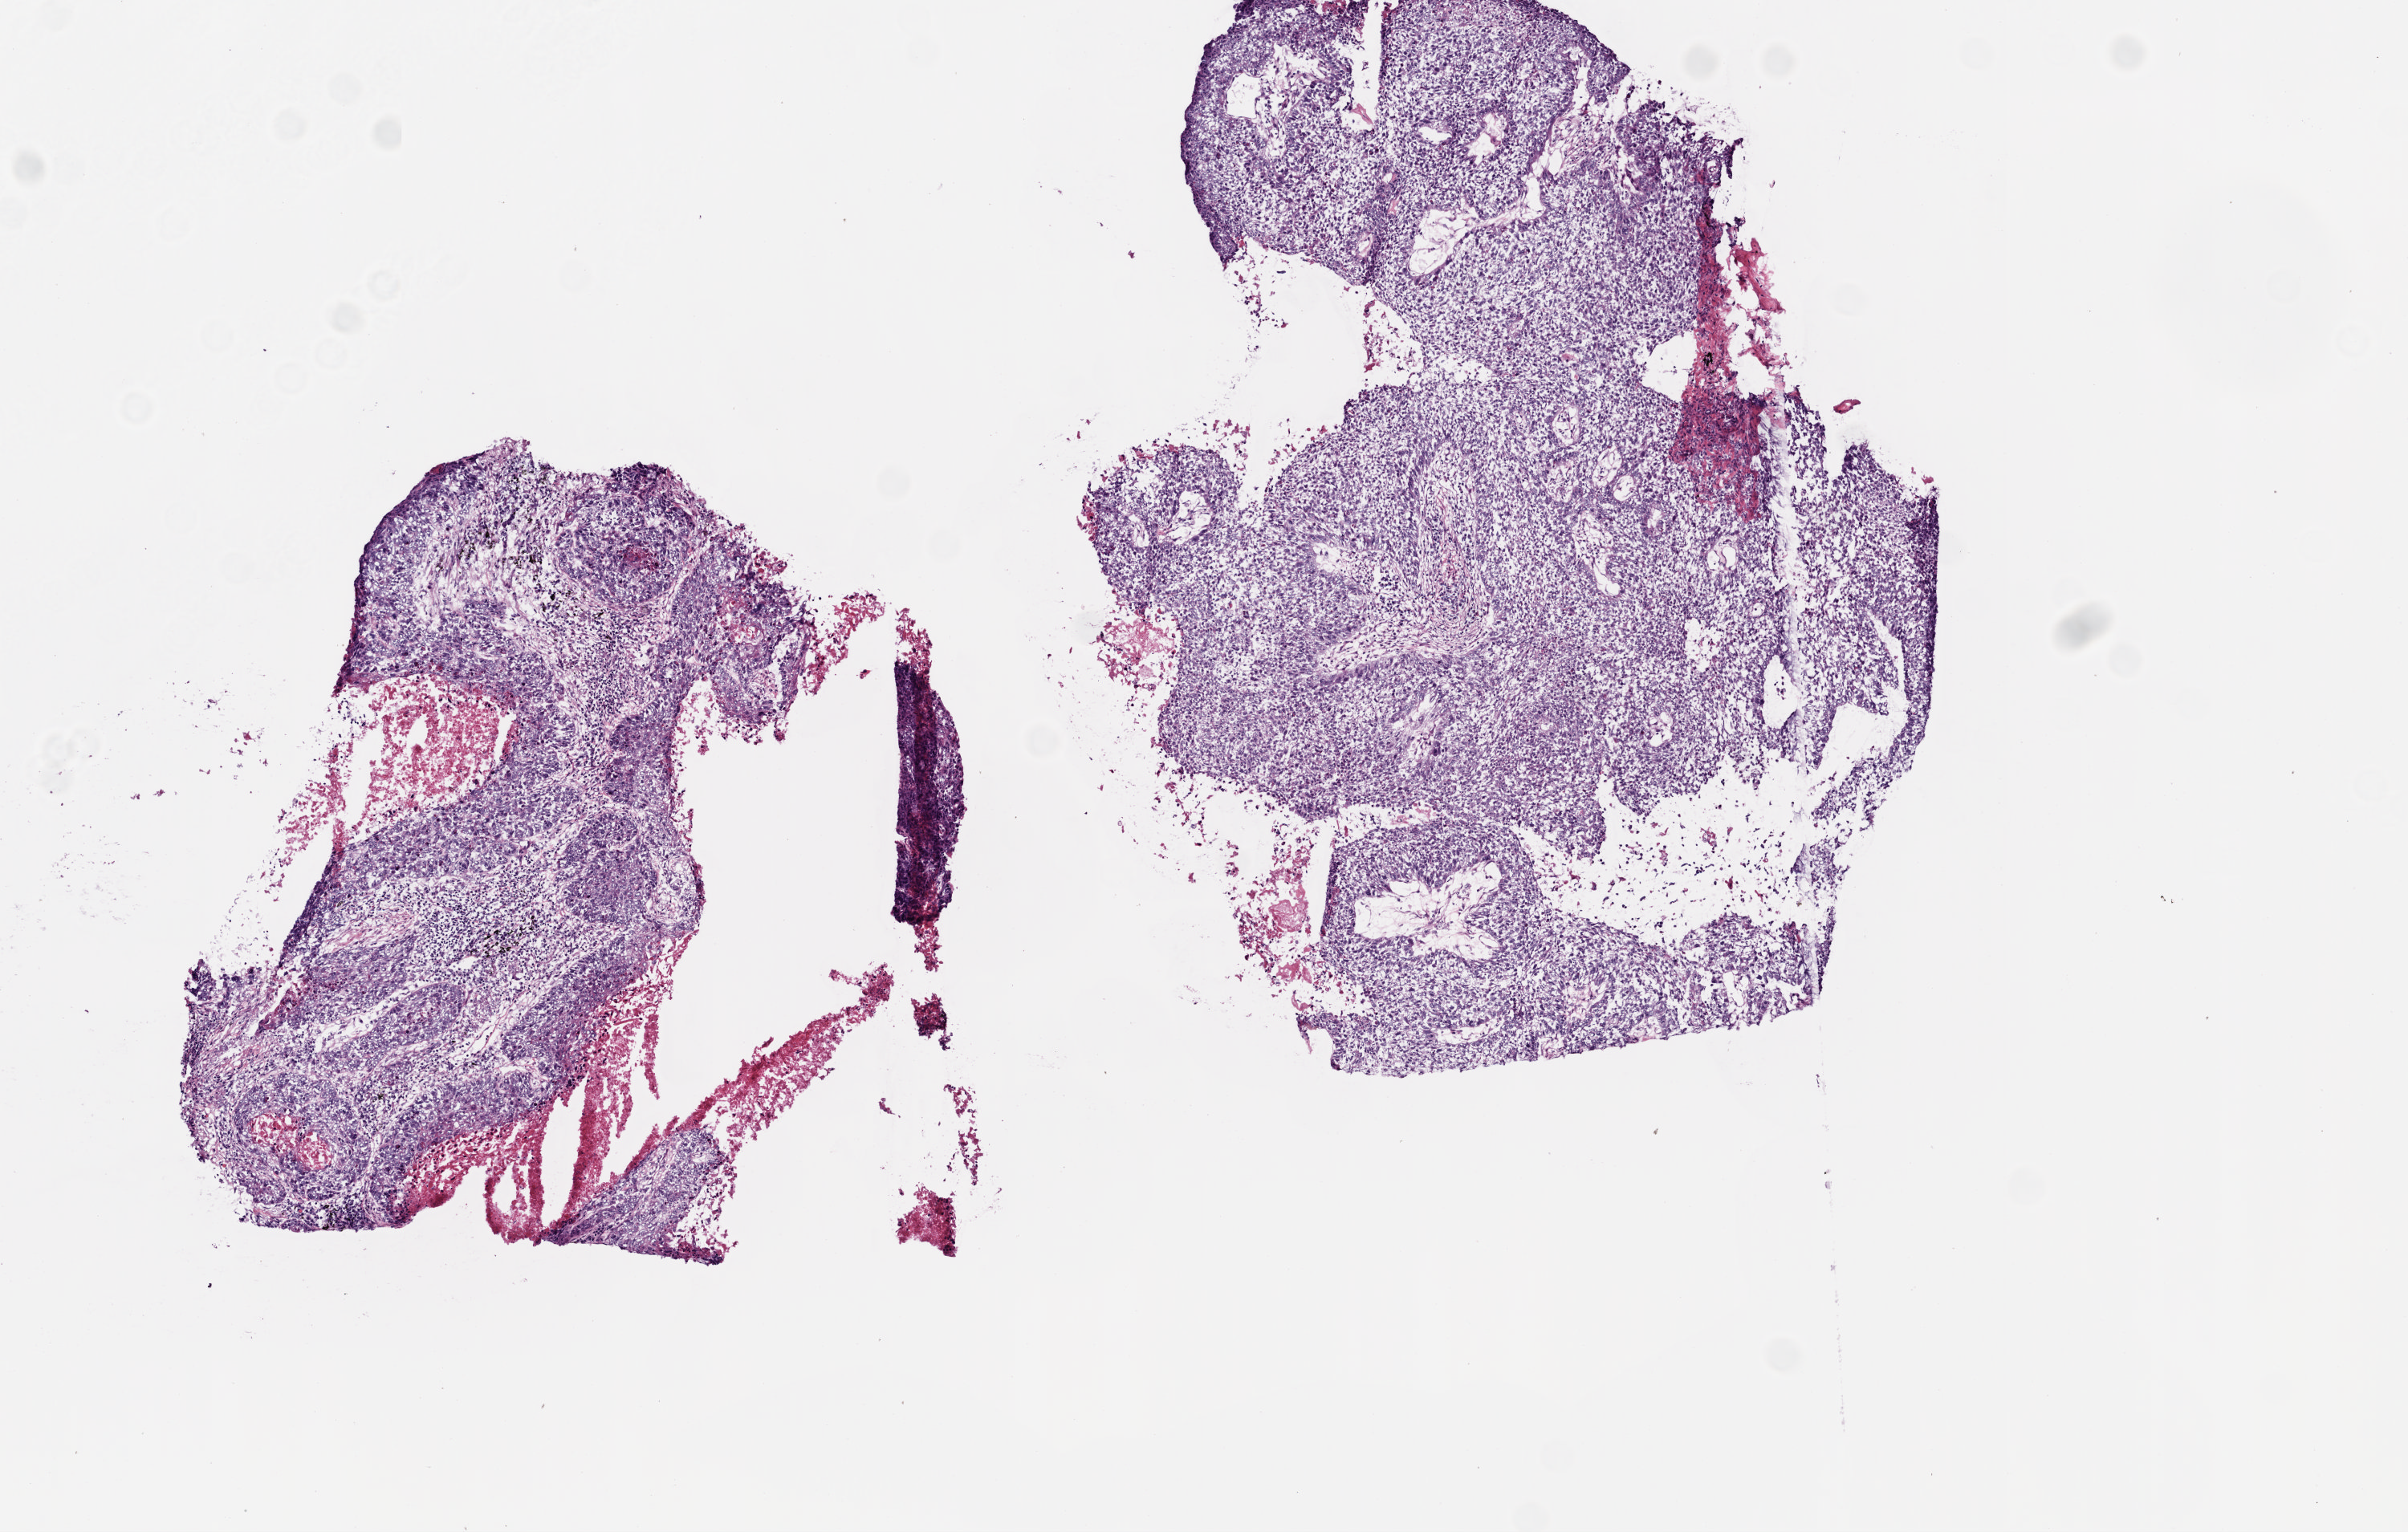
Digitized Hematoxylin and eosin (H&E) stained tissue section (whole slide), whole scanned area (about 6.0 x 3.8 mm, slide scanned at 20x) shown as a low-resolution overview, frozen section from the bottom of the tissue portion, primary tumour sample from the lung. Female patient; age at initial diagnosis 73 years. Pathologist review of this section (percent, as recorded): tumour cells 75%, tumour nuclei 70%, normal cells 0%, stromal cells 10%, necrosis 15%.
AJCC pathologic stage: IA. Pathologic diagnosis: Squamous cell carcinoma, NOS (upper lobe, lung).